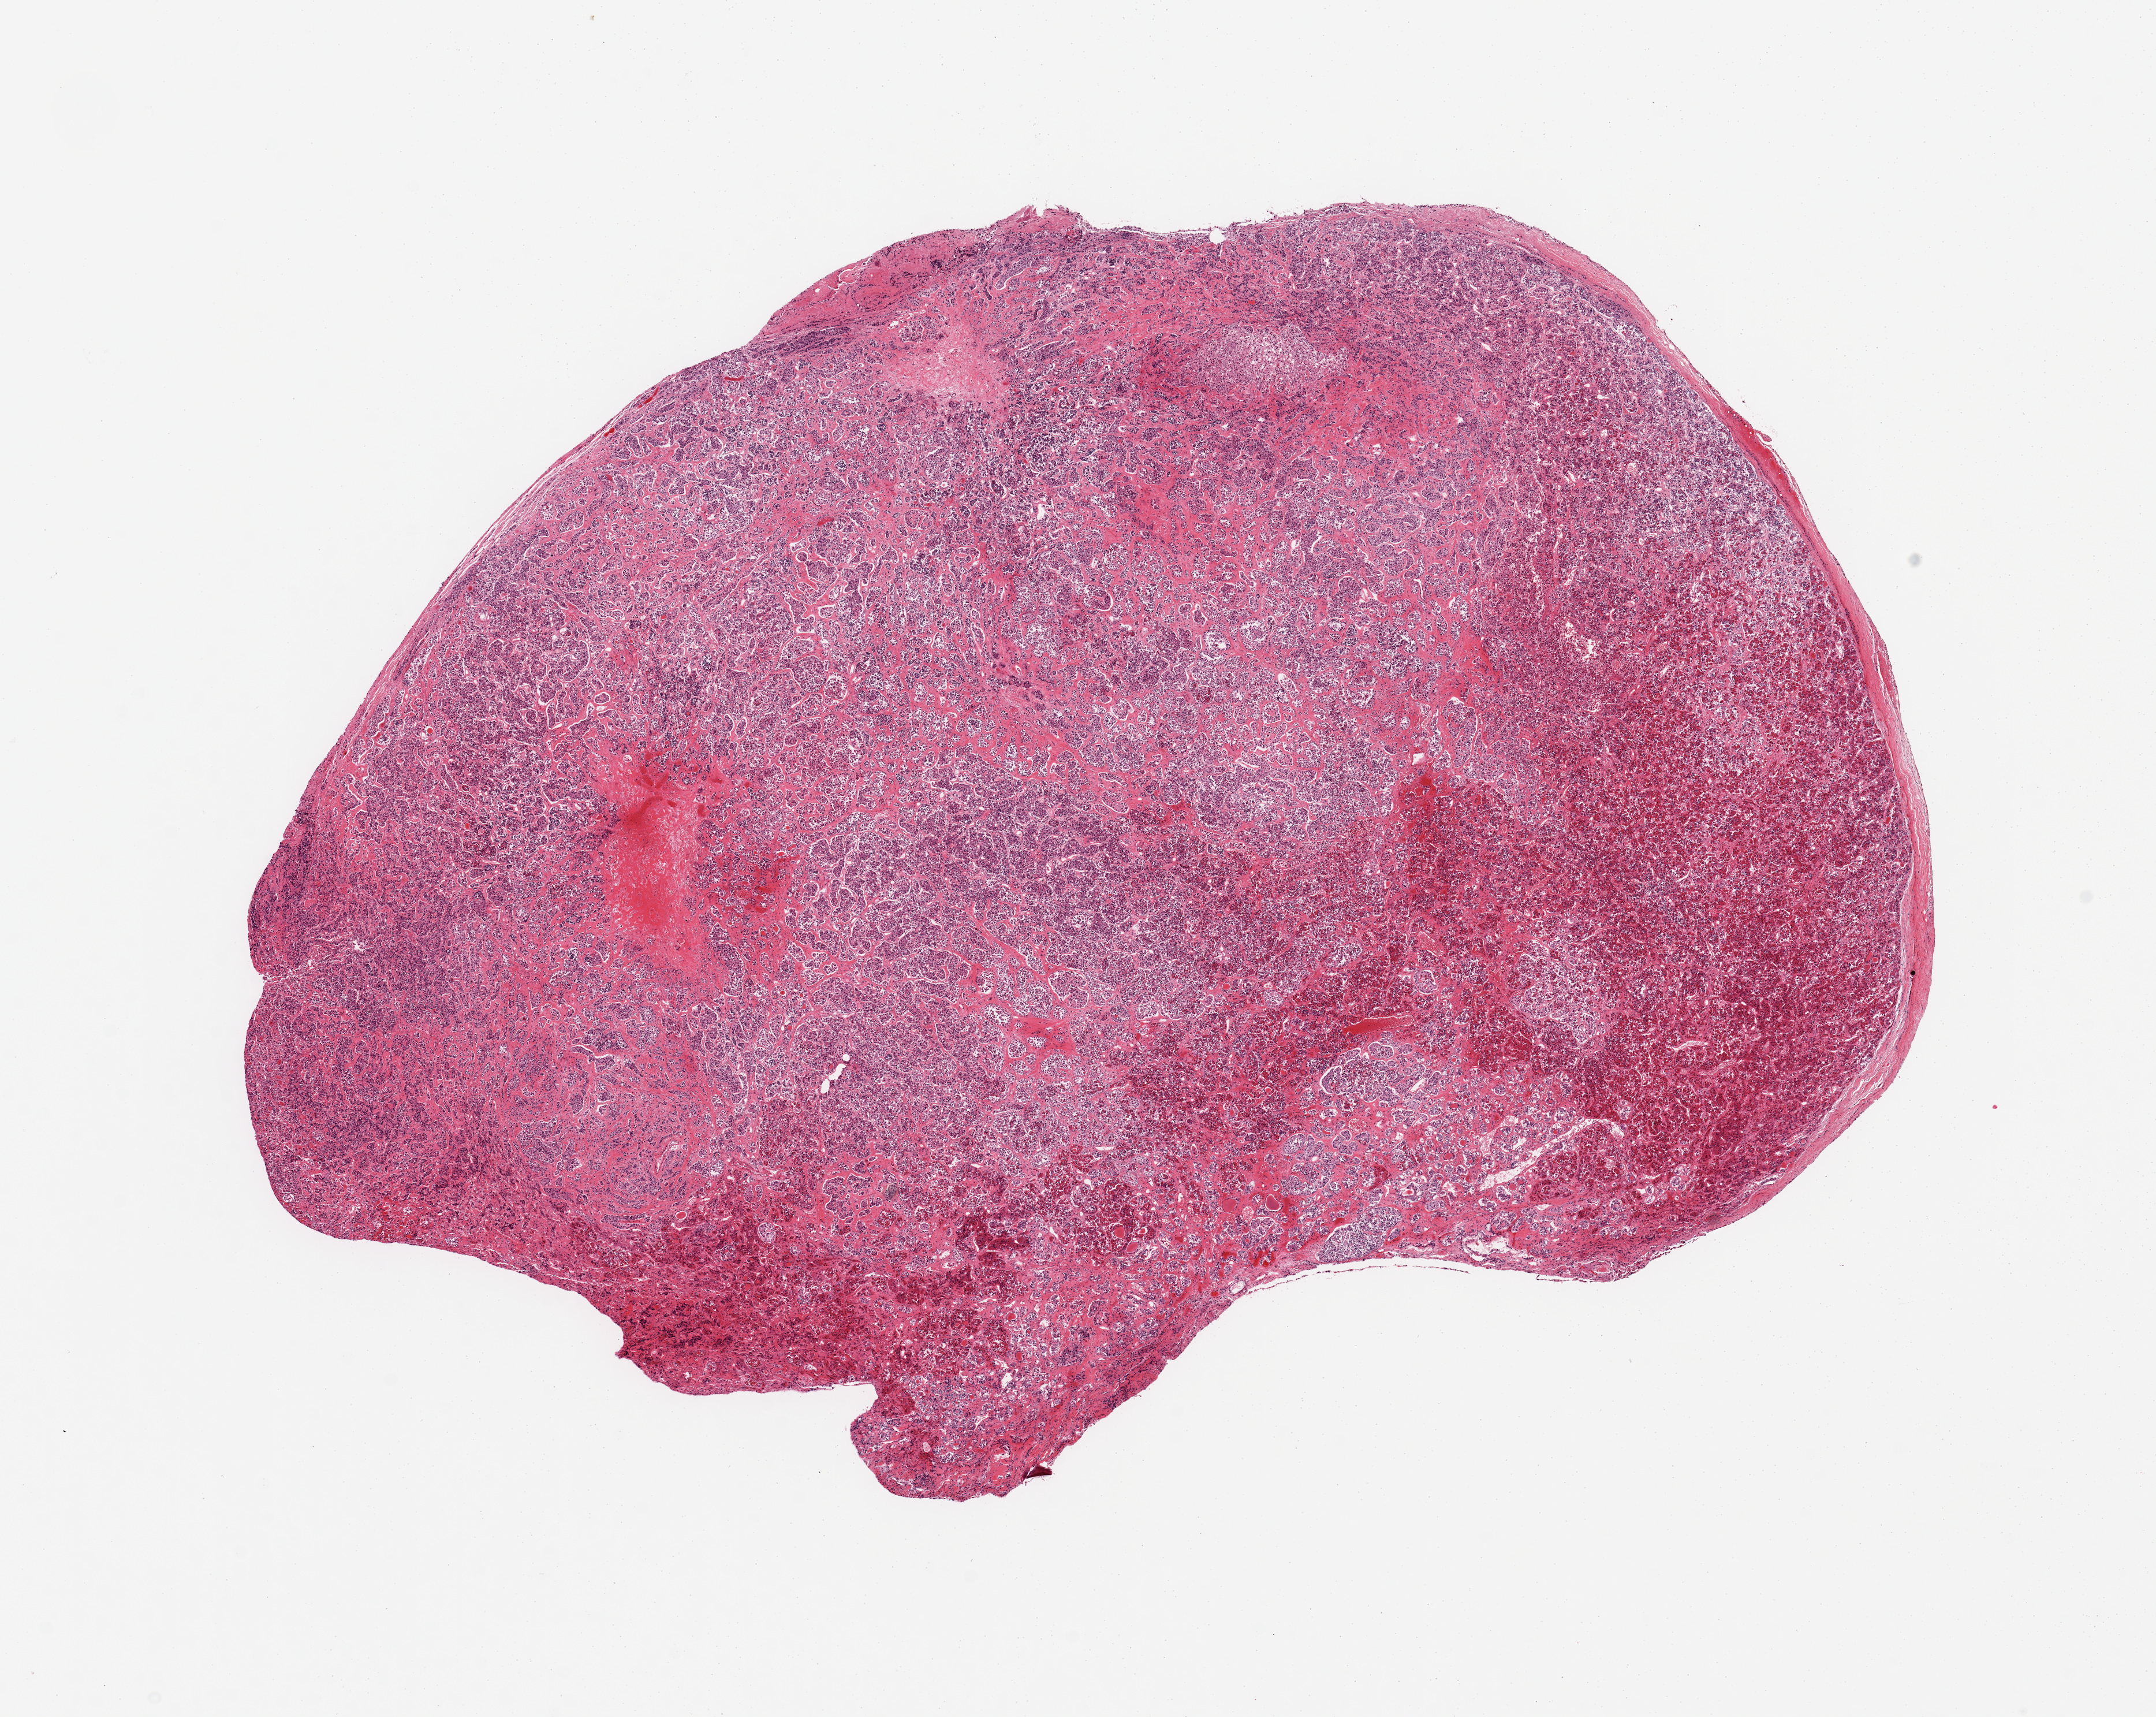
Digitized hematoxylin and eosin (H&E)-stained section, brightfield, low-resolution overview of the scanned area, about 14.8 x 11.8 mm. PAXgene-fixed, paraffin-embedded tissue. Section of pituitary (target tissue). Donor tissue sample. Donor sex: male.
Pathologist's review note for this sample: 1 piece; well dissected anterior portion.